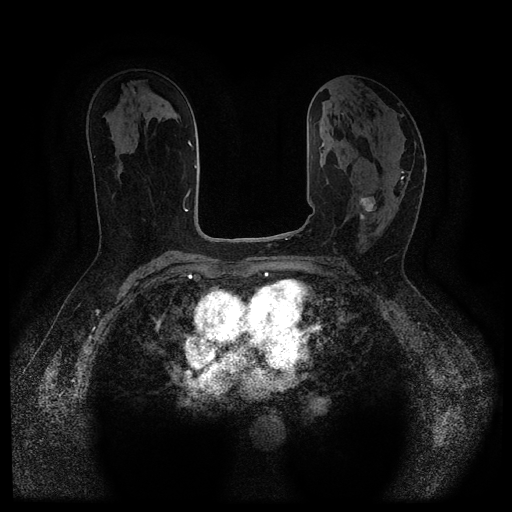
Breast MRI (dynamic contrast-enhanced, multi-phase), one axial slice. Slice 58 of 116 in the series (ordered by position). Dynamic contrast-enhanced series, time point 2 of 5 at this slice position (early post-contrast). 1.5 T. TE 2.6 ms, TR 5.4 ms. 2 mm slice thickness. 512 × 512 image matrix, field of view 340 × 340 mm. Patient: female, 64 years.
Structures marked on this image (semi-automatic segmentation, software-assisted and operator-edited):
- breast lesion (labelled 'tumour' in the annotation; benign lesions carry a separate 'benign' label): bounding box (x1, y1, x2, y2) in pixels: (357, 197, 376, 212)